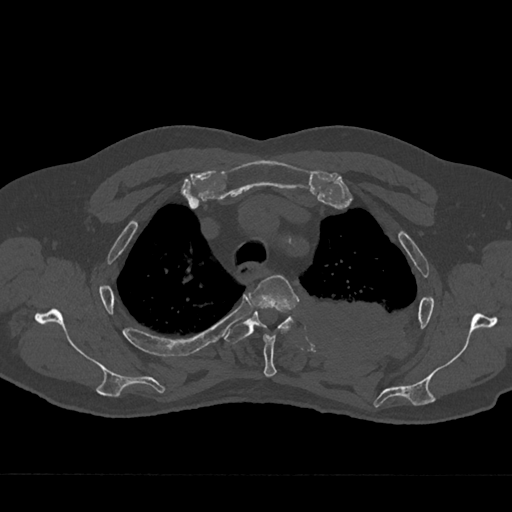
CT including the spine, one axial slice. Slice 545 of 797 in the series (ordered by position). Bone window (W 1800 / L 400 HU). 0.5 mm slice thickness. 512 × 512 image matrix, field of view 377 × 377 mm. Patient: male, 75 years. From the clinical record (not read from this slice): primary cancer: renal.
Structures marked on this image (semi-automatic segmentation, software-assisted and operator-edited):
- T3 vertebra: bounding box <249,275,299,377> (left, top, right, bottom; pixels)
- T4 vertebra: <224,311,294,344>